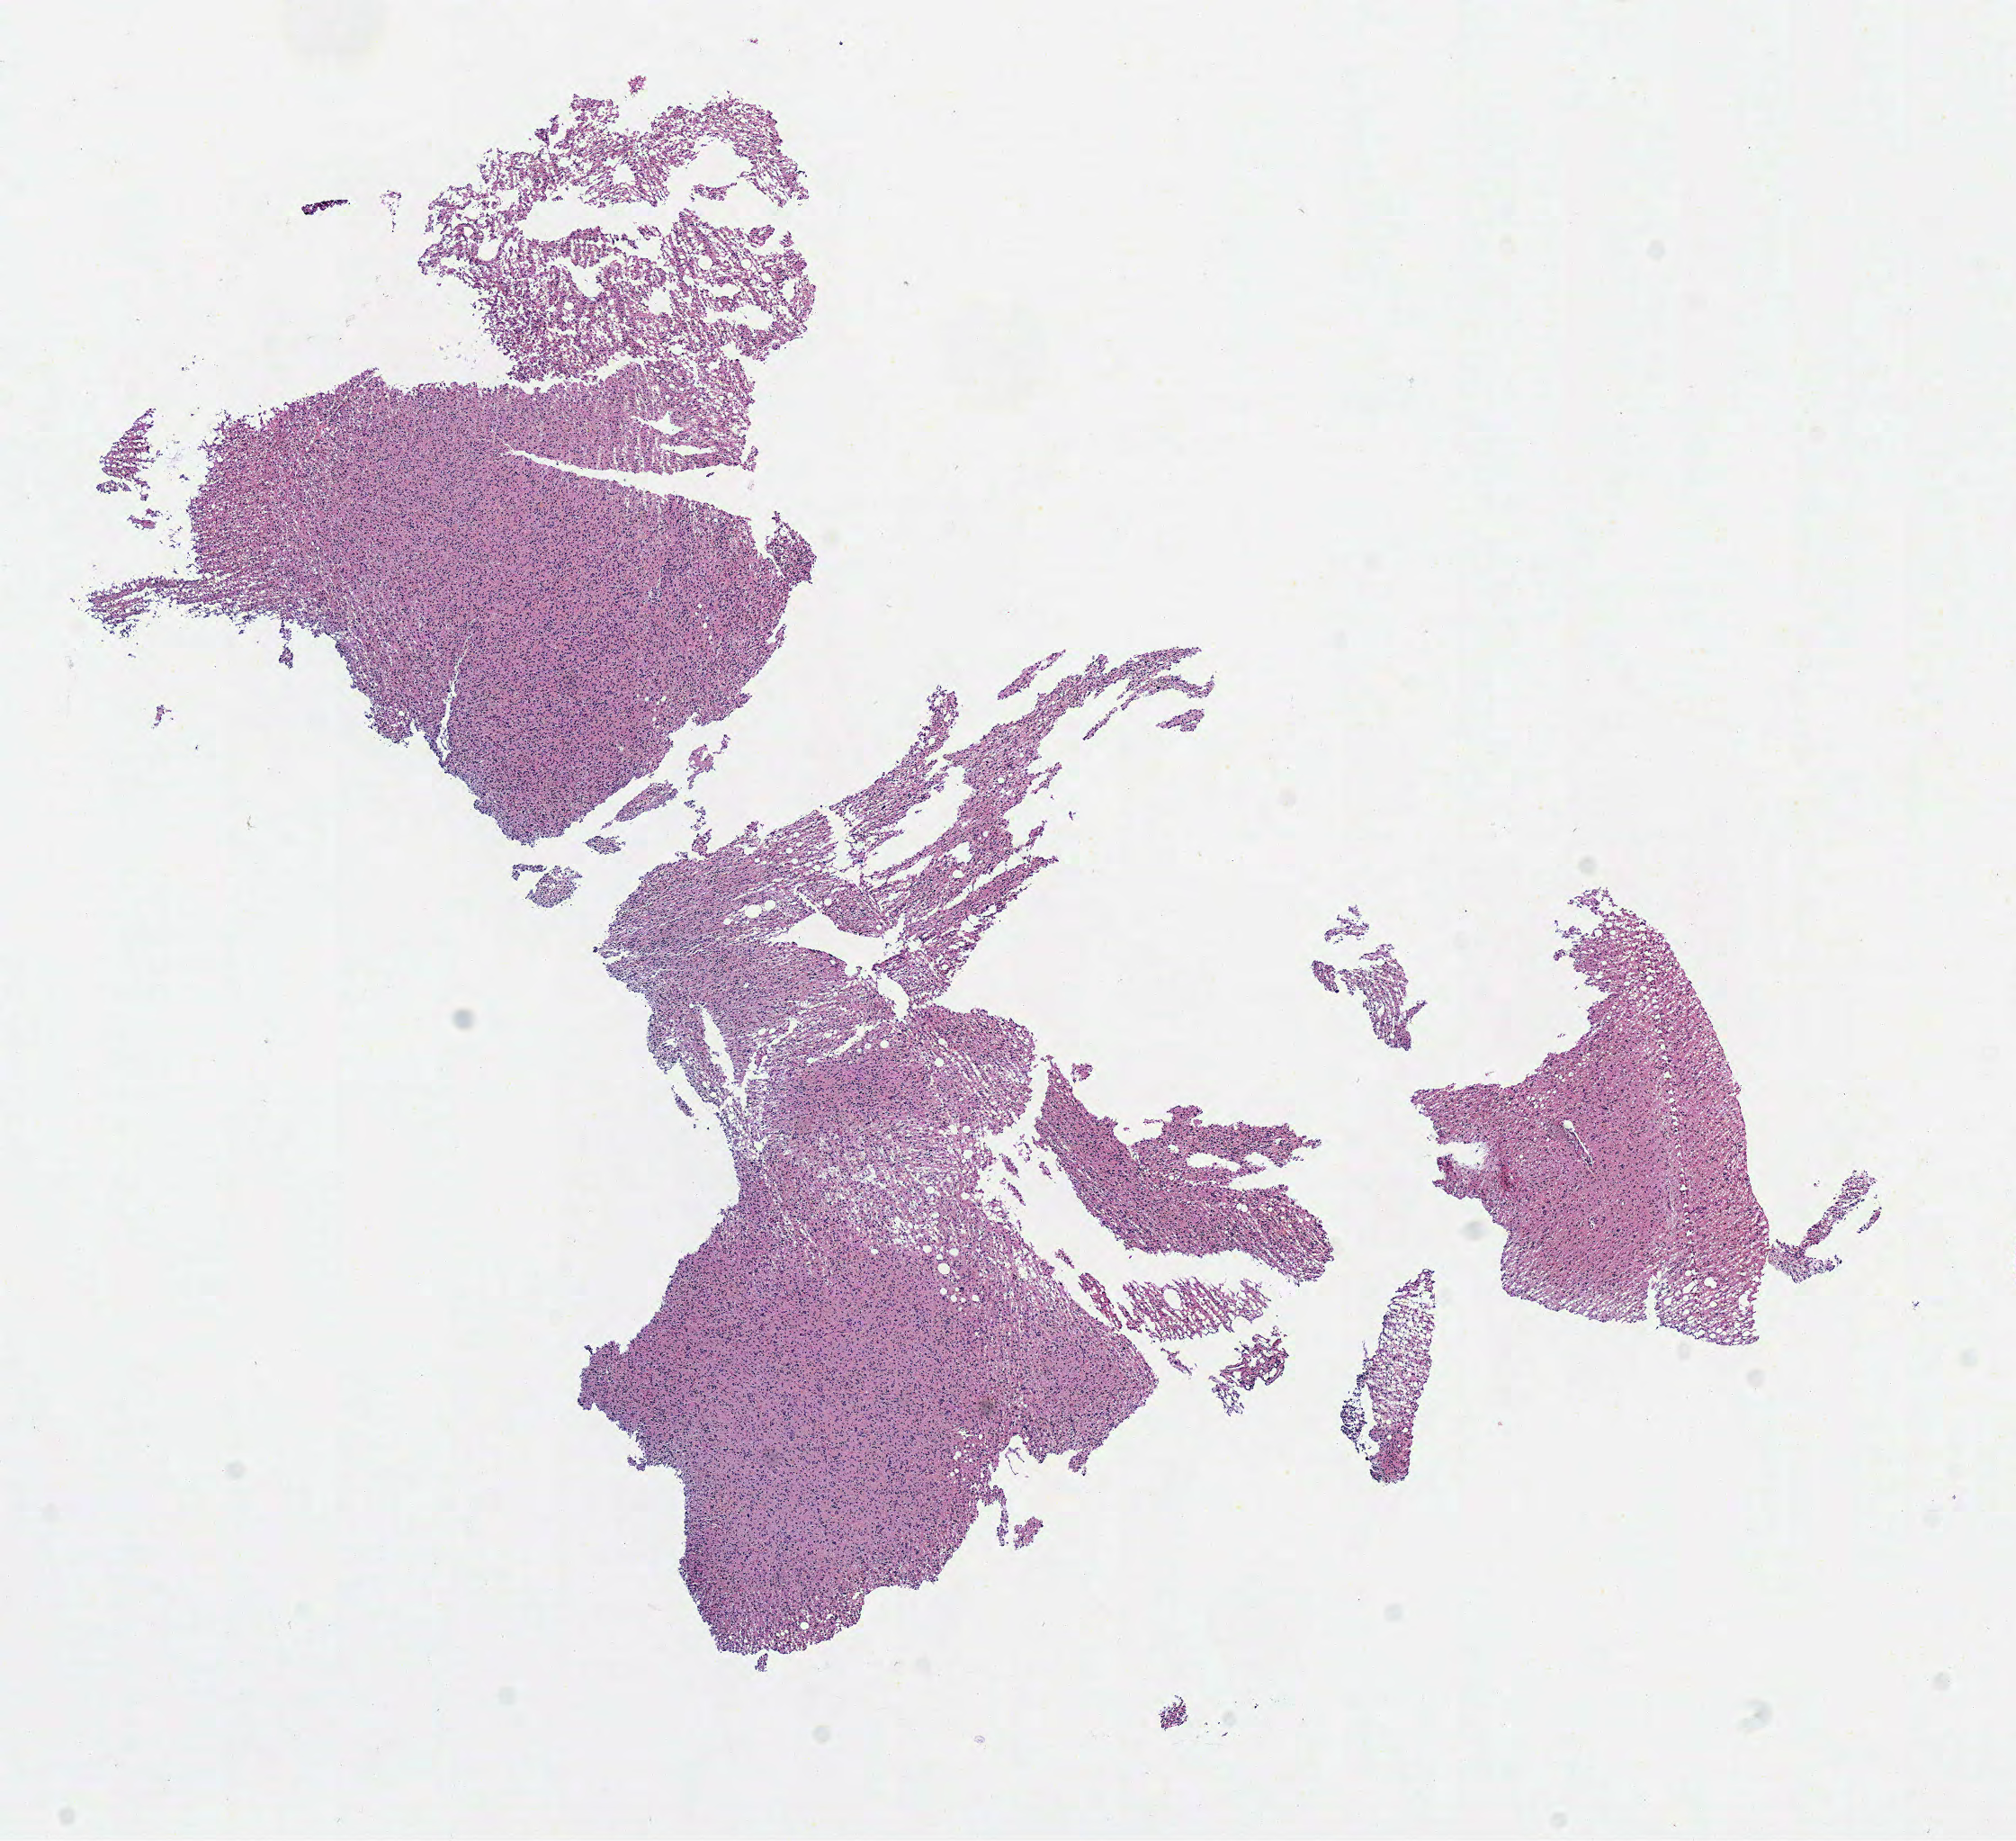
Whole-slide histology image, Hematoxylin and eosin (H&E) stained, whole scanned area (about 8.8 x 8.0 mm, from a 40x scan) shown as a low-resolution overview, frozen section, brain, primary tumour sample. Female, age 60 years at initial diagnosis. Histologic grade: G3 (poorly differentiated). Slide review estimates, as recorded: tumour cells 100%, tumour nuclei 80%, normal cells 0%, stromal cells 0%, necrosis 0%.
Laterality: right. Histologic diagnosis: Mixed glioma (cerebrum).